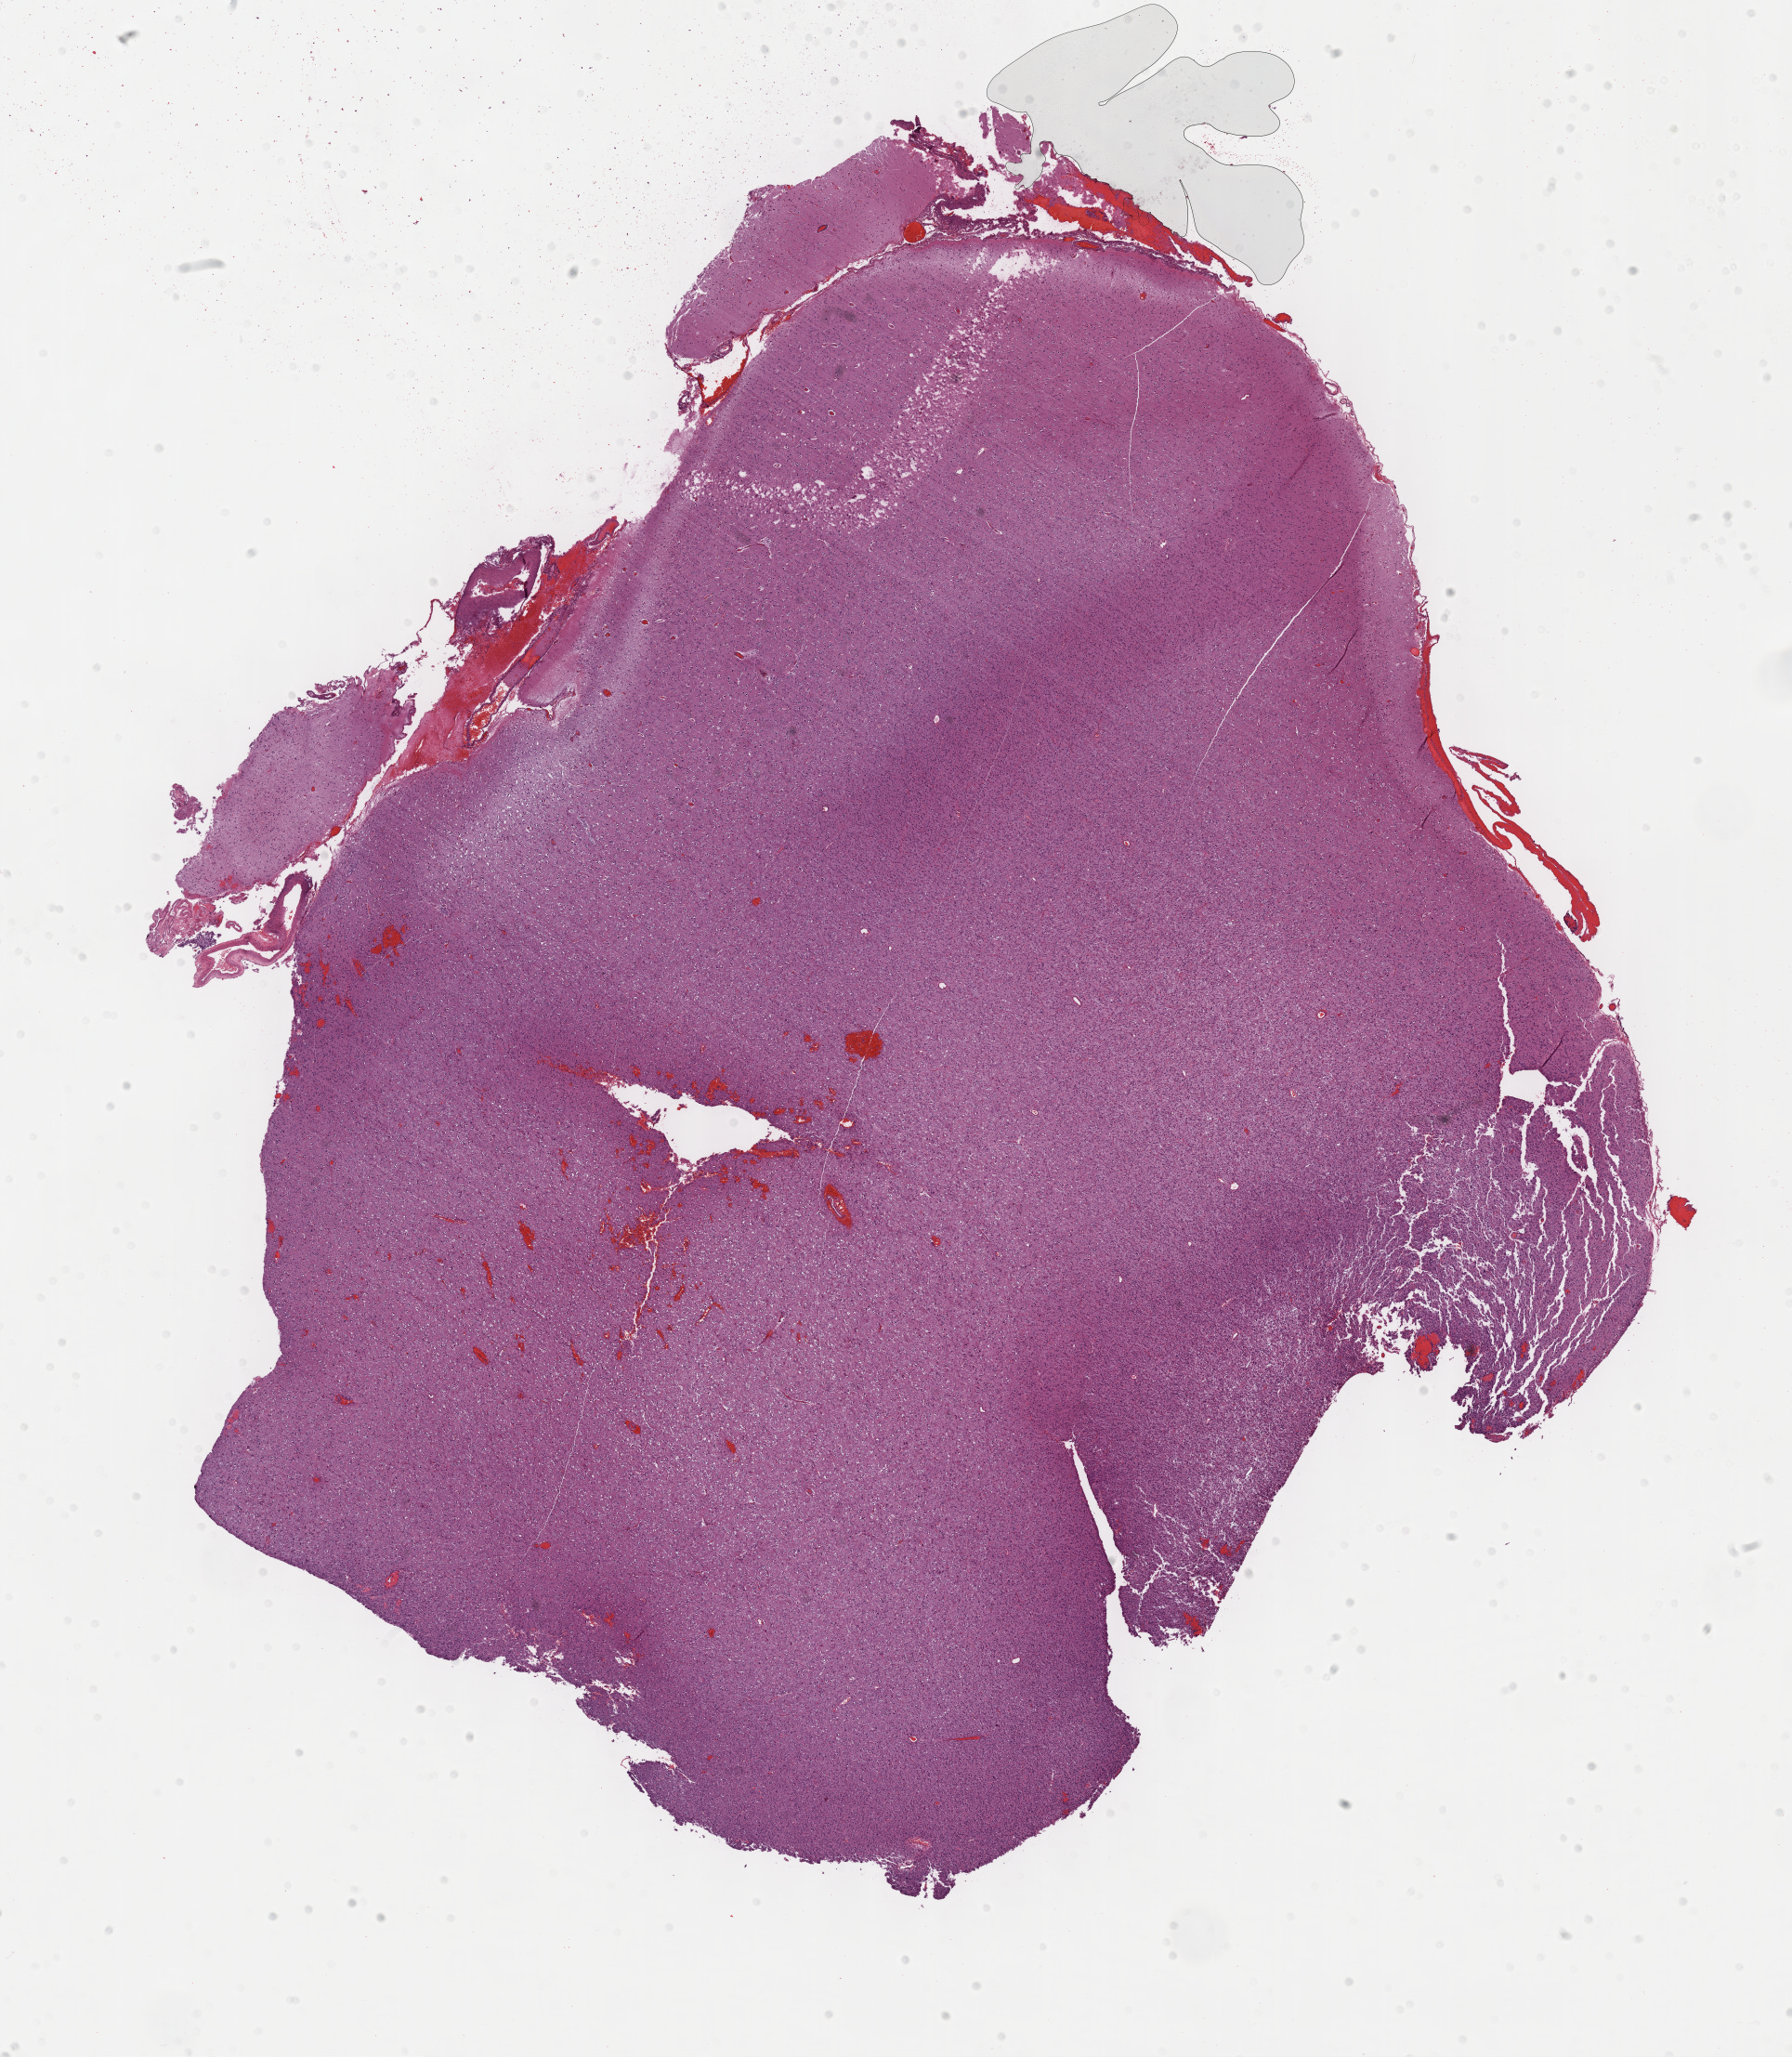
Digitized H&E-stained tissue section (whole slide), low-resolution overview of the scanned area, about 15.6 x 17.9 mm (slide scanned at 40x). Formalin-fixed paraffin-embedded (FFPE) diagnostic section. Sample: primary tumour, brain. Patient: male, age at initial diagnosis 29 years. Histologic grade: G3 (poorly differentiated).
Pathologic diagnosis: Mixed glioma (cerebrum).